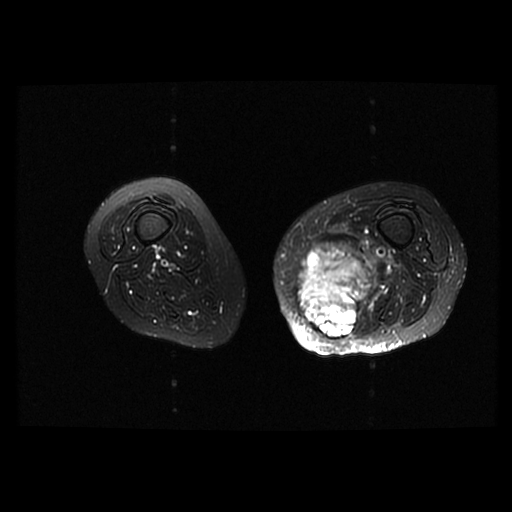
MRI of an extremity soft-tissue mass, one axial slice. Slice 25 of 42 in the series (ordered by position). T2-weighted fat-saturated. 6 mm slice thickness. 512 × 512 image matrix, field of view 420 × 420 mm. Female patient. From the clinical record (not read from this slice): histological type: pleomorphic leiomyosarcoma; grade: high; site of the primary tumour: left thigh.
Outlined on this slice (expert manual segmentation):
- gross tumour volume including surrounding oedema: bounding box [x1, y1, x2, y2] px = [297, 243, 380, 338]
- gross tumour volume (mass): [297, 243, 373, 338]